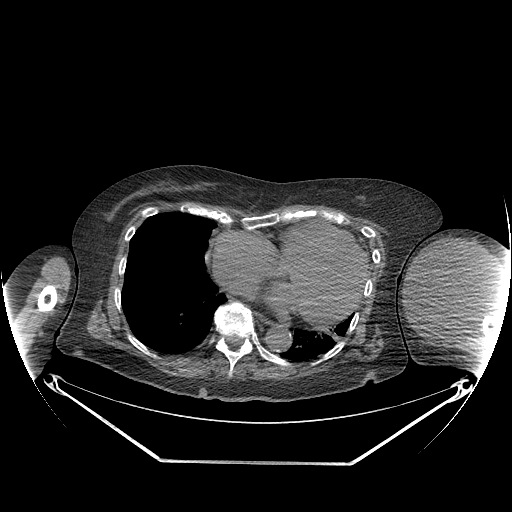
CT of an extremity soft-tissue mass (from a PET/CT study), one axial slice; position 157 of 267 along the scan axis; reconstruction kernel STANDARD; 140 kVp; soft-tissue window (W 400 / L 40 HU); 512 × 512 image matrix, field of view 500 × 500 mm. Female patient. Case-level facts recorded for this patient, not image findings: histological type: pleiomorphic leiomyosarcoma; grade: high; site of the primary tumour: left biceps.
Structures marked on this image (expert contour drawn on MRI and transferred to this co-registered scan by the dataset authors):
- gross tumour volume including surrounding oedema: bounding box <404,237,496,330> (left, top, right, bottom; pixels)
- gross tumour volume (mass): <404,240,496,328>